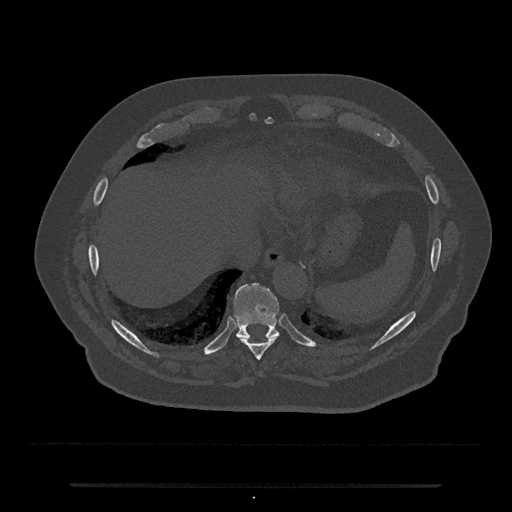
CT including the spine, one axial slice; position 734 of 797 along the scan axis; bone window (W 1800 / L 400 HU); 0.5 mm slice thickness; 512 × 512 image matrix, field of view 434 × 434 mm. Patient: male, 80 years. From the clinical record (not read from this slice): primary cancer: prostate.
Outlined on this slice (semi-automatic segmentation, software-assisted and operator-edited):
- T10 vertebra: box from (x=233, y=283) to (x=280, y=338) px
- T9 vertebra: (x=239, y=337)–(x=278, y=360)